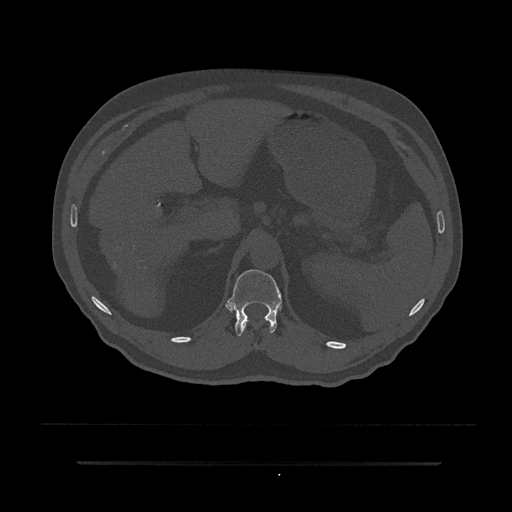
CT including the spine, one axial slice; slice 225 of 797 in the series (ordered by position); bone window (W 1800 / L 400 HU); 512 × 512 image matrix. Patient: male, 59 years. From the clinical record (not read from this slice): primary cancer: bile ducts; vertebrae with lytic lesions (as recorded): T10.
Annotated regions visible in this slice (semi-automatically segmented with operator editing):
- T12 vertebra: bounding box (x1, y1, x2, y2) in pixels: (227, 269, 282, 336)